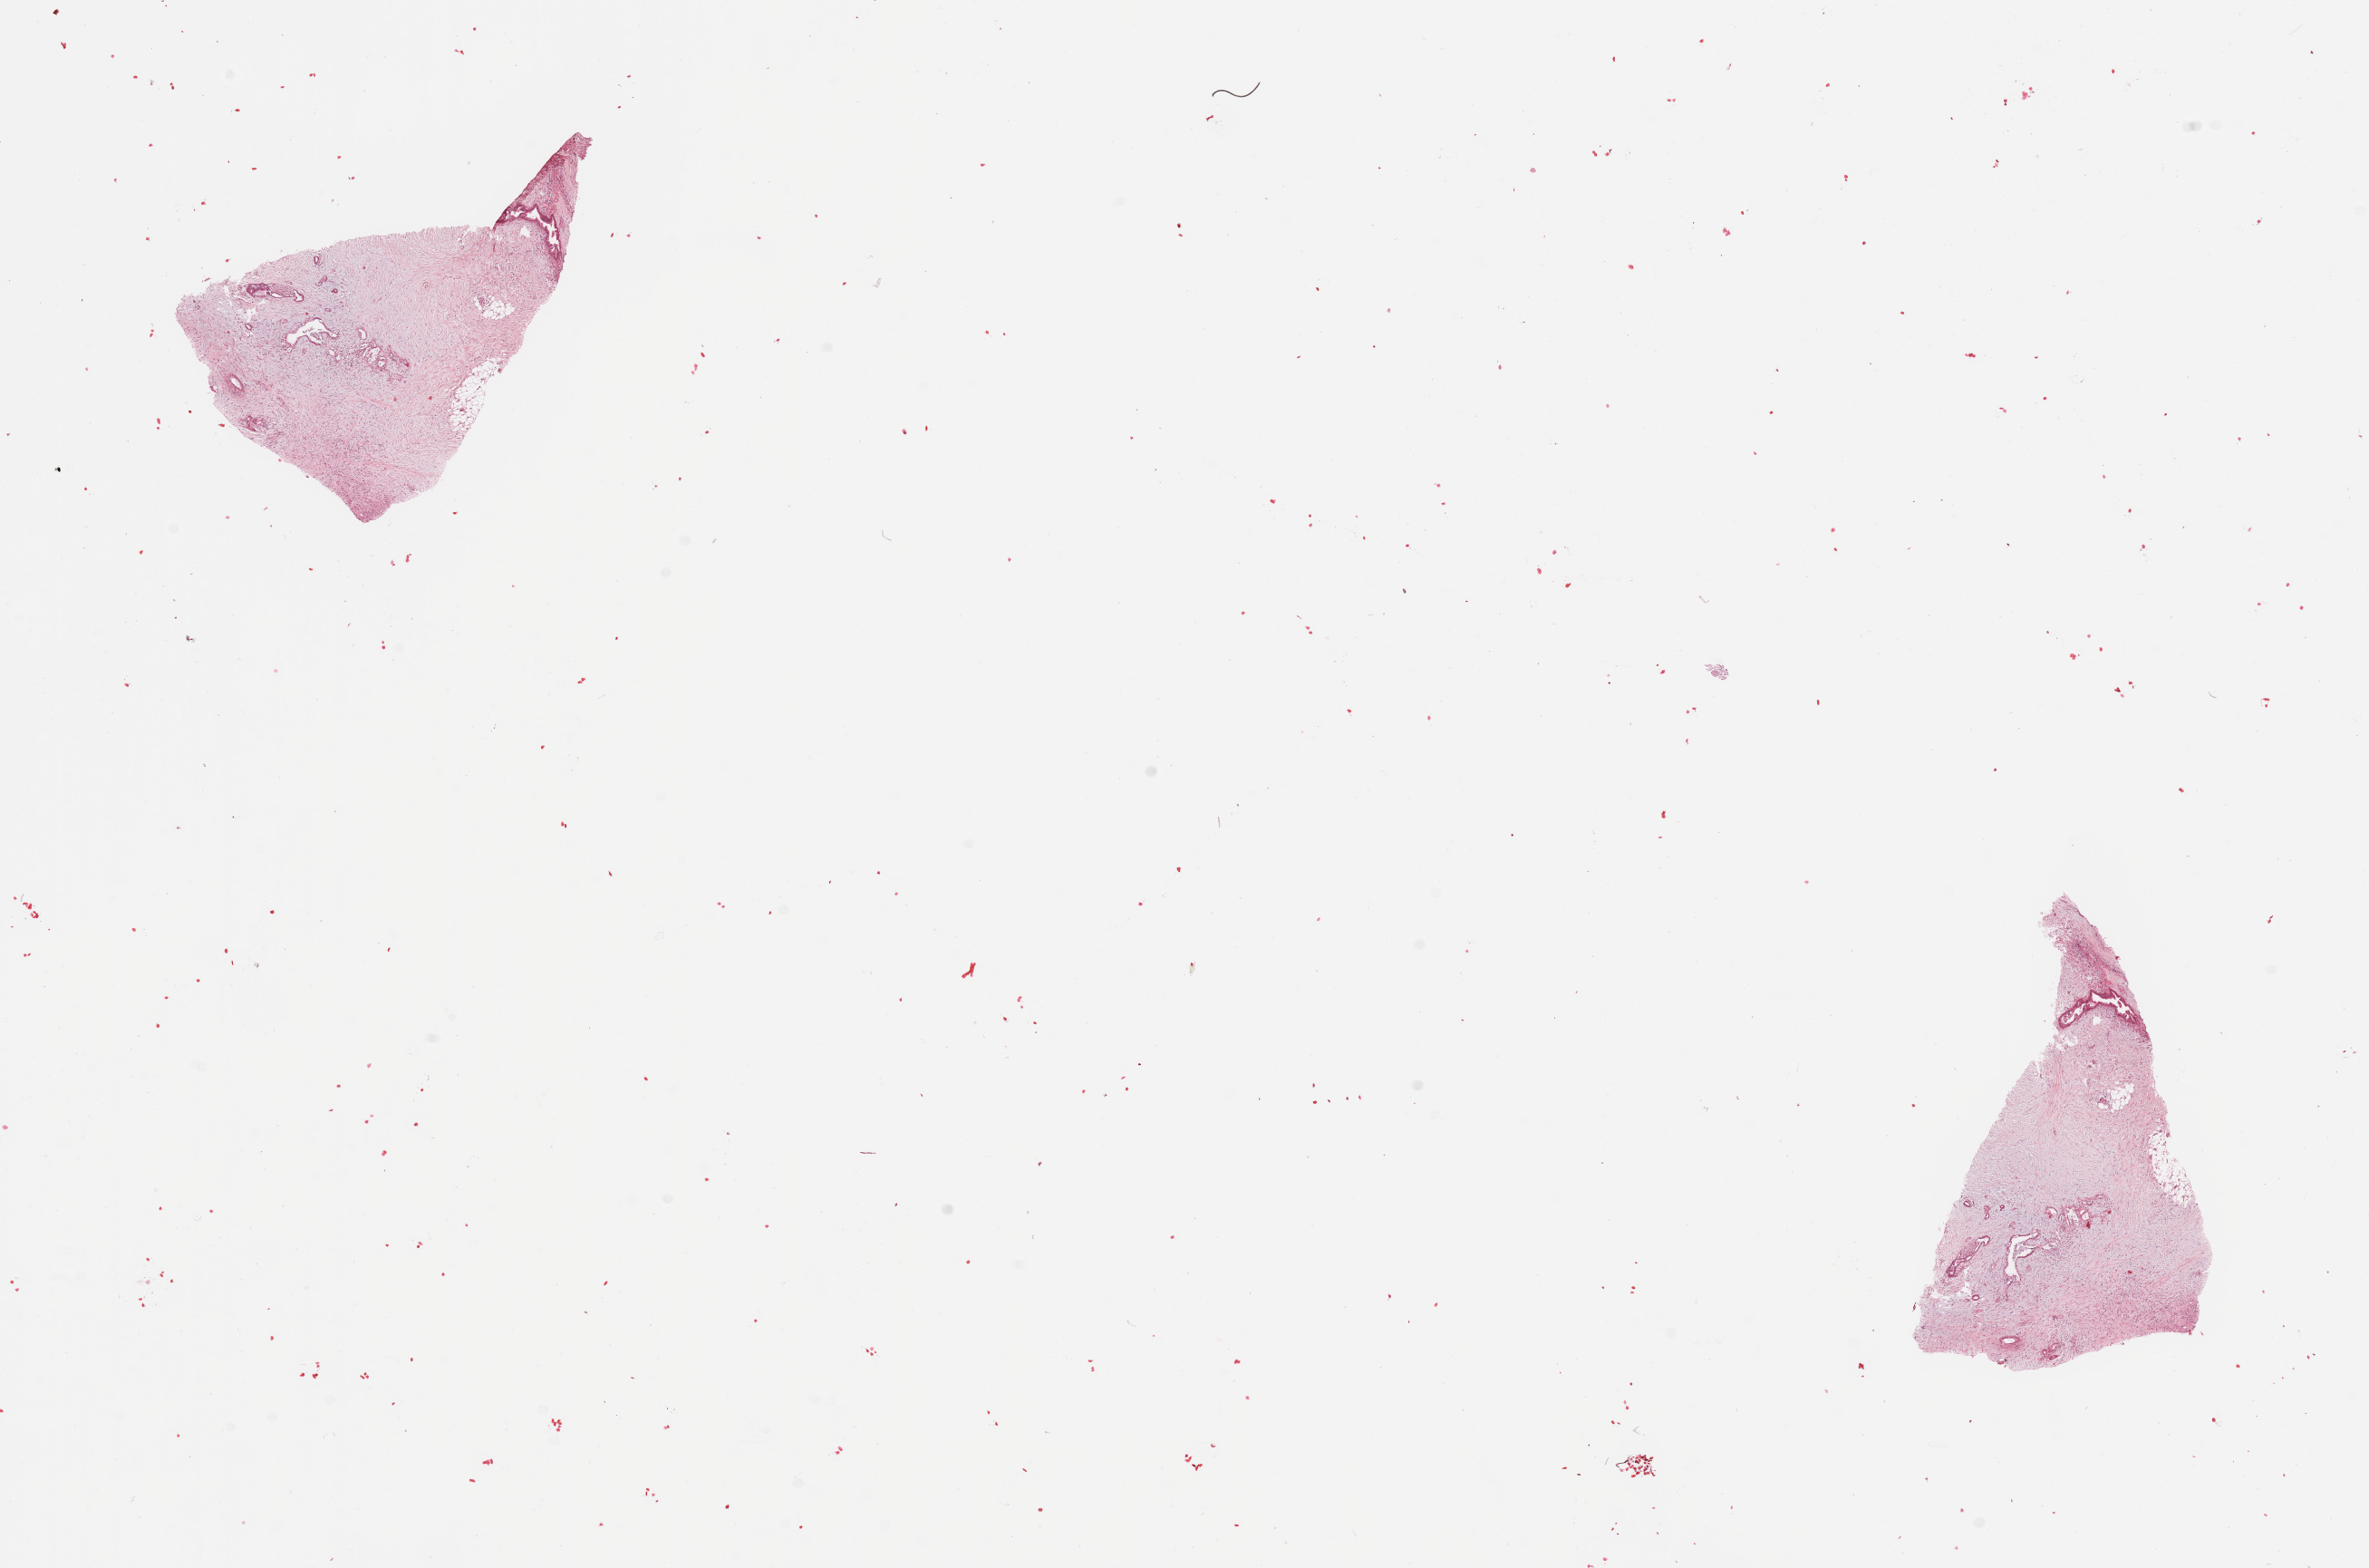
H&E whole-slide image — whole scanned area (about 20.7 x 13.7 mm, slide scanned at 20x) shown as a low-resolution overview, tumour tissue sample, pancreas. Female, 45 y/o. Histologic grade: G2 (moderately differentiated).
* histologic diagnosis: Infiltrating duct carcinoma, NOS
* AJCC pathologic stage: IIB
* primary tumour site (as recorded): head